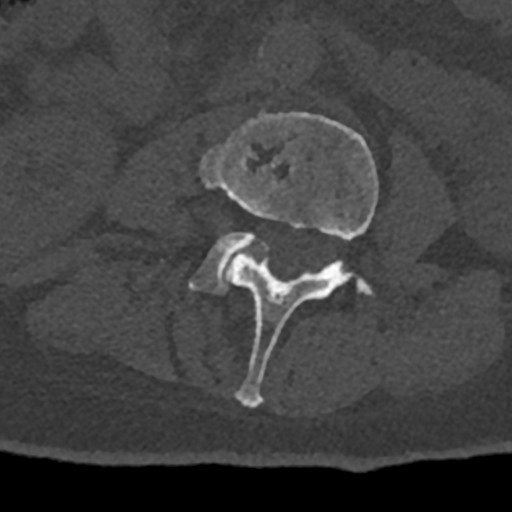
CT including the spine, one axial slice. Slice 307 of 797 in the series (ordered by position). Reconstruction kernel Br40s/3. 120 kVp. Bone window (W 1800 / L 400 HU). 0.5 mm slice thickness. 512 × 512 image matrix, field of view 160 × 160 mm. Male patient, age 74 years. From the clinical record (not read from this slice): primary cancer: renal; vertebrae with lytic lesions (as recorded): T10, L1, L2, L3, L4, L5.
Outlined on this slice (semi-automatic segmentation, software-assisted and operator-edited):
- L3 vertebra: bounding box (x1, y1, x2, y2) in pixels: (200, 113, 378, 408)
- L4 vertebra: (190, 231, 268, 294)